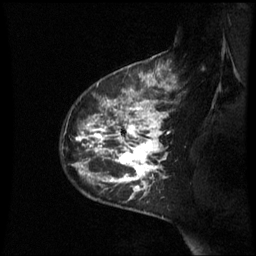
Breast MRI (dynamic contrast-enhanced), one sagittal slice. Position 45 of 60 along the scan axis. Dynamic contrast-enhanced series, image 2 of 3 at this slice position (ordered by acquisition). 1.5 T. TE 4.2 ms, TR 8.9 ms. 2.4 mm slice thickness. 256 × 256 image matrix, field of view 210 × 210 mm. Patient: female, 42 years. Case-level facts recorded for this patient, not image findings: setting: breast cancer imaged before/during neoadjuvant chemotherapy; receptor status: HER2-positive.
Annotated regions visible in this slice (semi-automatically segmented with operator editing):
- analysis volume of interest (the breast-tissue region the enhancement analysis was run in; not a lesion): bounding box [x1, y1, x2, y2] px = [63, 93, 170, 210]
- tumour enhancement mask (voxels above the 70 % enhancement threshold inside the analysis volume of interest): [78, 93, 169, 201]